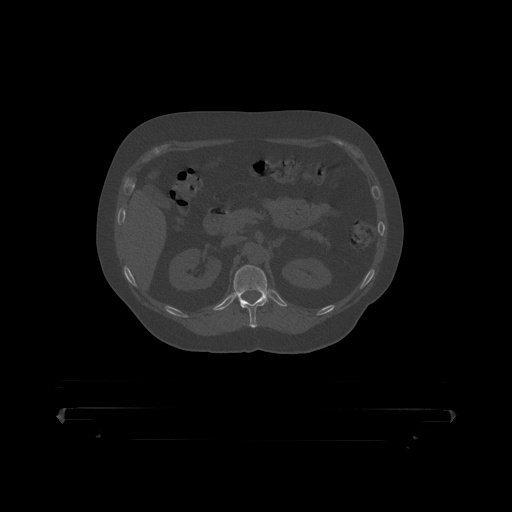
CT including the spine, one axial slice. Position 168 of 390 along the scan axis. Reconstruction kernel STANDARD. 120 kVp. Bone window (W 1800 / L 400 HU). 1.25 mm slice thickness. 512 × 512 image matrix, field of view 650 × 650 mm. Male patient, age 60 years. Case-level facts recorded for this patient, not image findings: primary cancer: prostate.
Outlined on this slice (semi-automatic segmentation, software-assisted and operator-edited):
- T12 vertebra: bounding box (x1, y1, x2, y2) in pixels: (234, 265, 270, 319)